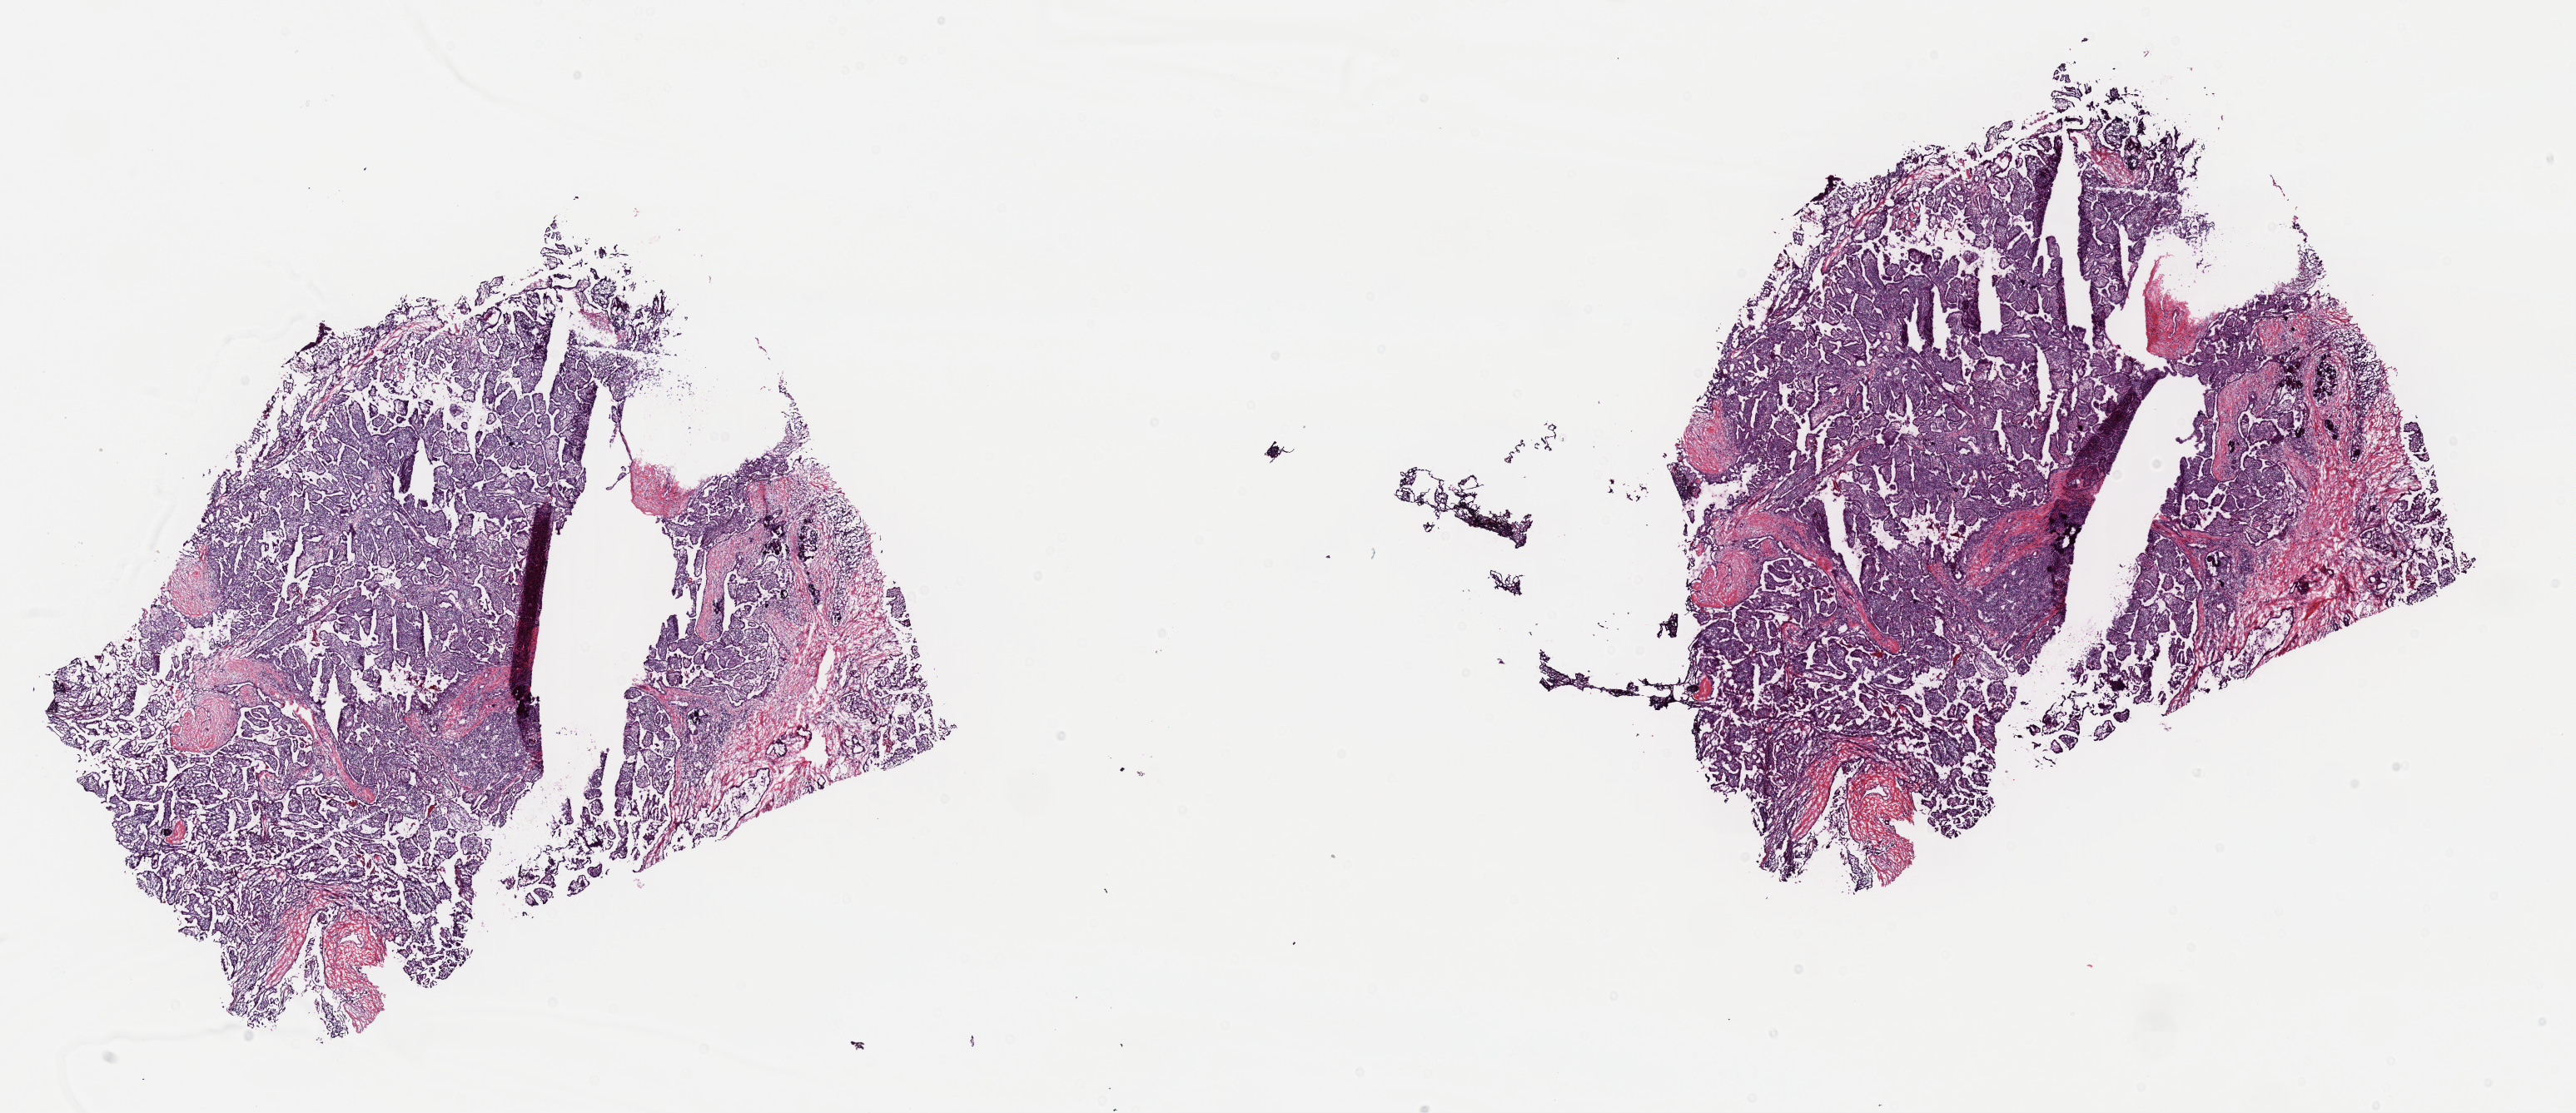
Whole-slide histology image, H&E-stained, a low-resolution overview of the entire scanned area, about 24.4 x 10.6 mm (from a 40x scan). Frozen section from the top of the tissue portion. Thyroid, primary tumour sample. Female, age 18 years at initial diagnosis. Composition of this section per pathologist review: tumour cells 80%, tumour nuclei 85%, normal cells 0%, stromal cells 20%, necrosis 0%. Infiltration values recorded for this section: lymphocyte infiltration 30%, monocyte infiltration 8%, neutrophil infiltration 0%.
Laterality: right. AJCC pathologic stage: I. Diagnosis: Papillary adenocarcinoma, NOS (thyroid gland). Lymph nodes positive (case pathology): 11 of 14 examined.